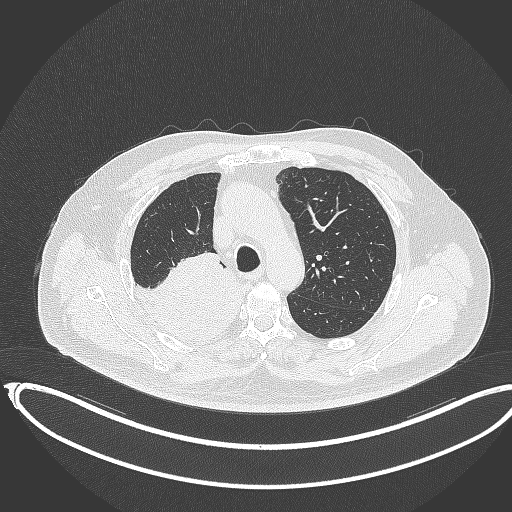
Chest CT, one axial slice. 120 kVp. Lung window (W 1500 / L -600 HU). 1 mm slice thickness. 512 × 512 image matrix, field of view 436 × 436 mm. Male patient, age 68 years. Case-level facts recorded for this patient, not image findings: clinical TNM (as recorded): T2a N0 M0.
Outlined on this slice (rectangle marked by the reading radiologist):
- lung tumour (recorded histology: adenocarcinoma): box from (x=130, y=253) to (x=243, y=346) px